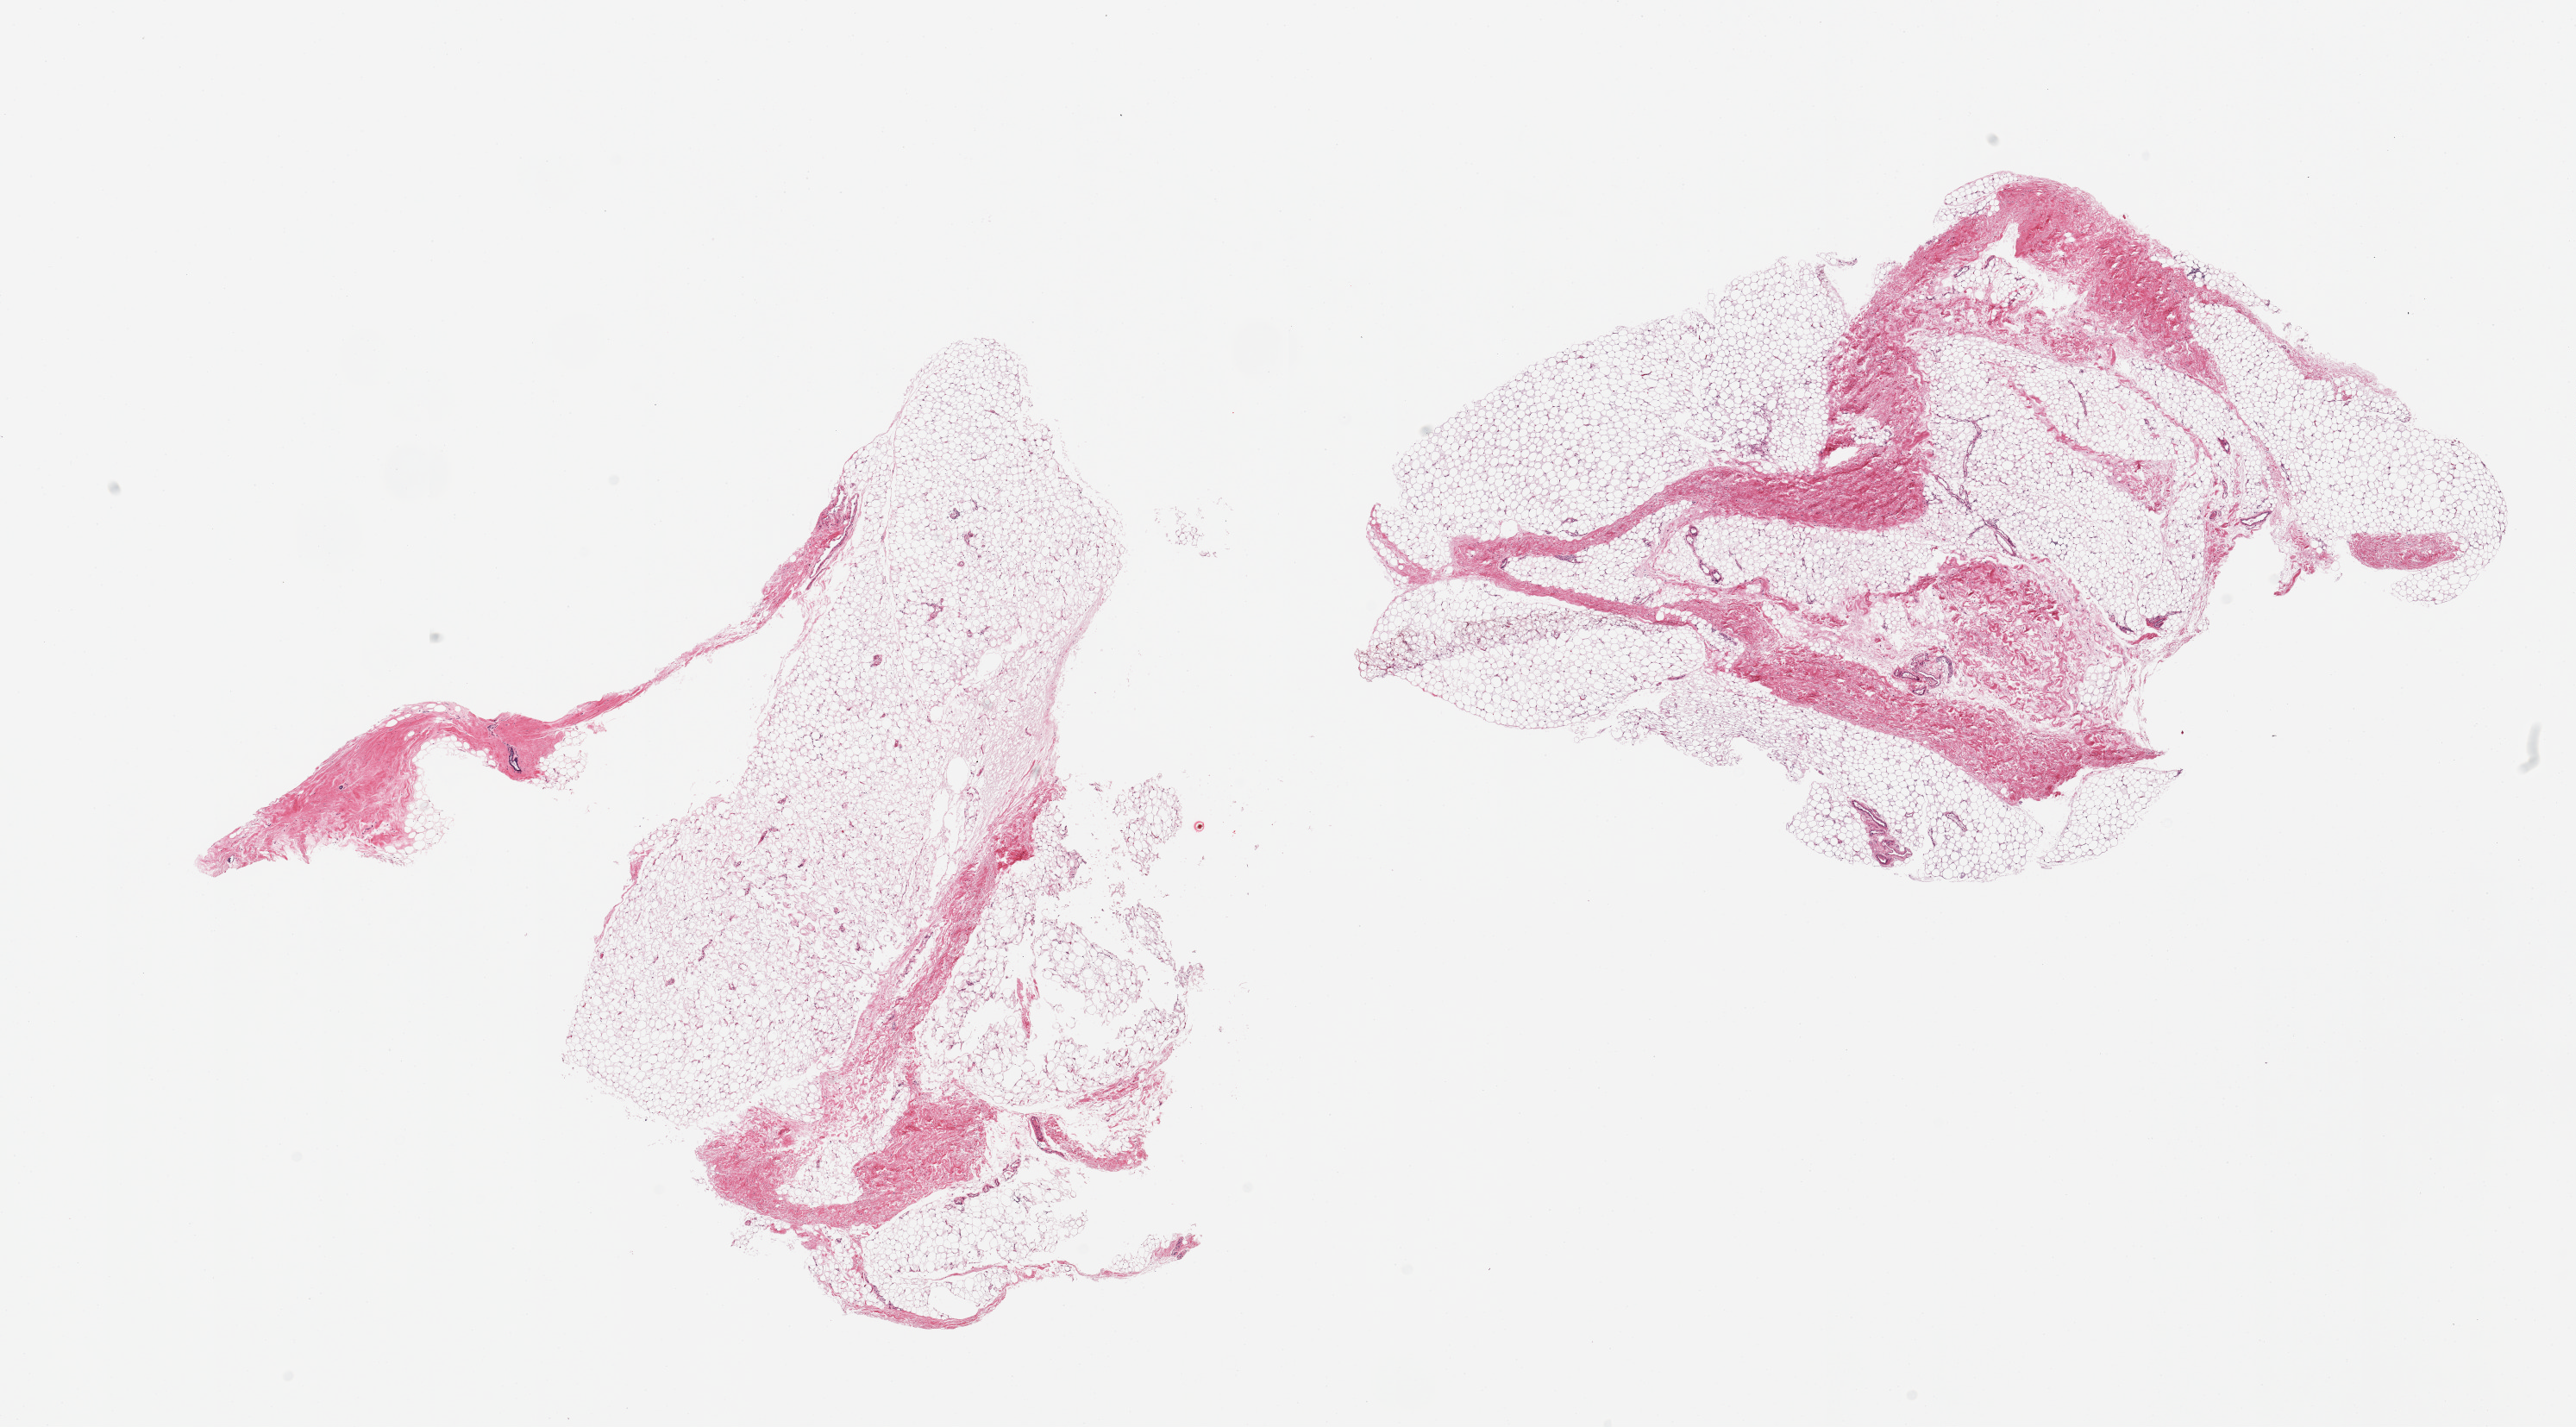
Digitized H&E-stained section, brightfield — shown as a low-resolution overview of the whole scanned area (about 23.6 x 13.1 mm, slide scanned at 20x). PAXgene-fixed, paraffin-embedded tissue. Section of breast (target tissue). Tissue donor sample. Donor: male.
Review note (as recorded): 2 pieces; predominantly fat with fibrous tissue with rare duct.